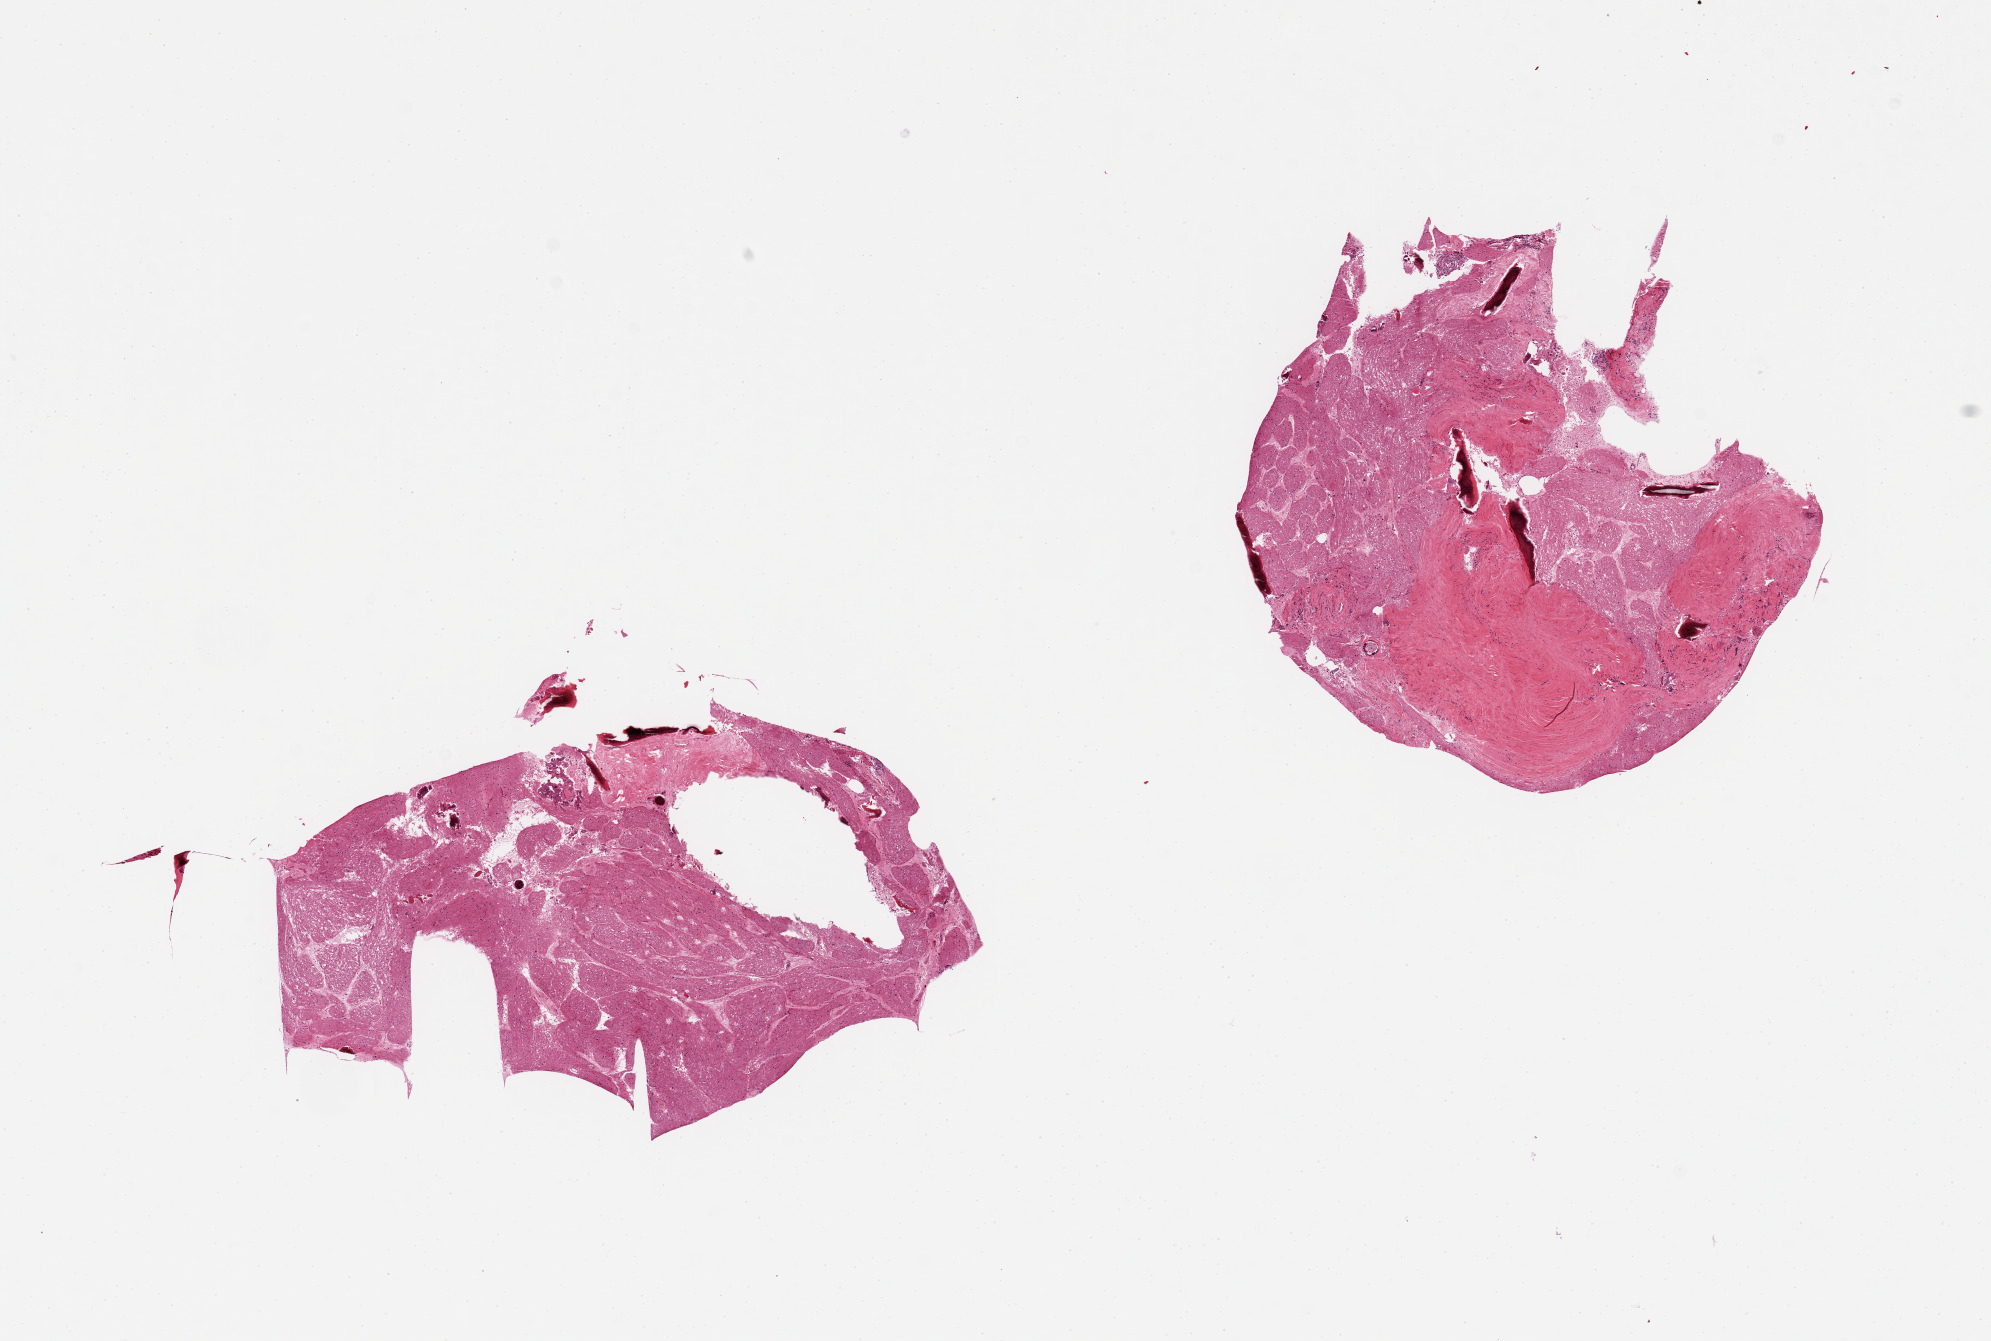
Digitized H&E-stained section, brightfield — whole scanned area (about 15.8 x 10.6 mm) shown as a low-resolution overview; PAXgene-fixed, paraffin-embedded tissue; target tissue: pituitary; donor tissue sample. Male donor.
Reviewer comment on this tissue sample: 2 pieces, marked autolysis, clacified debris/fibrous tissue.